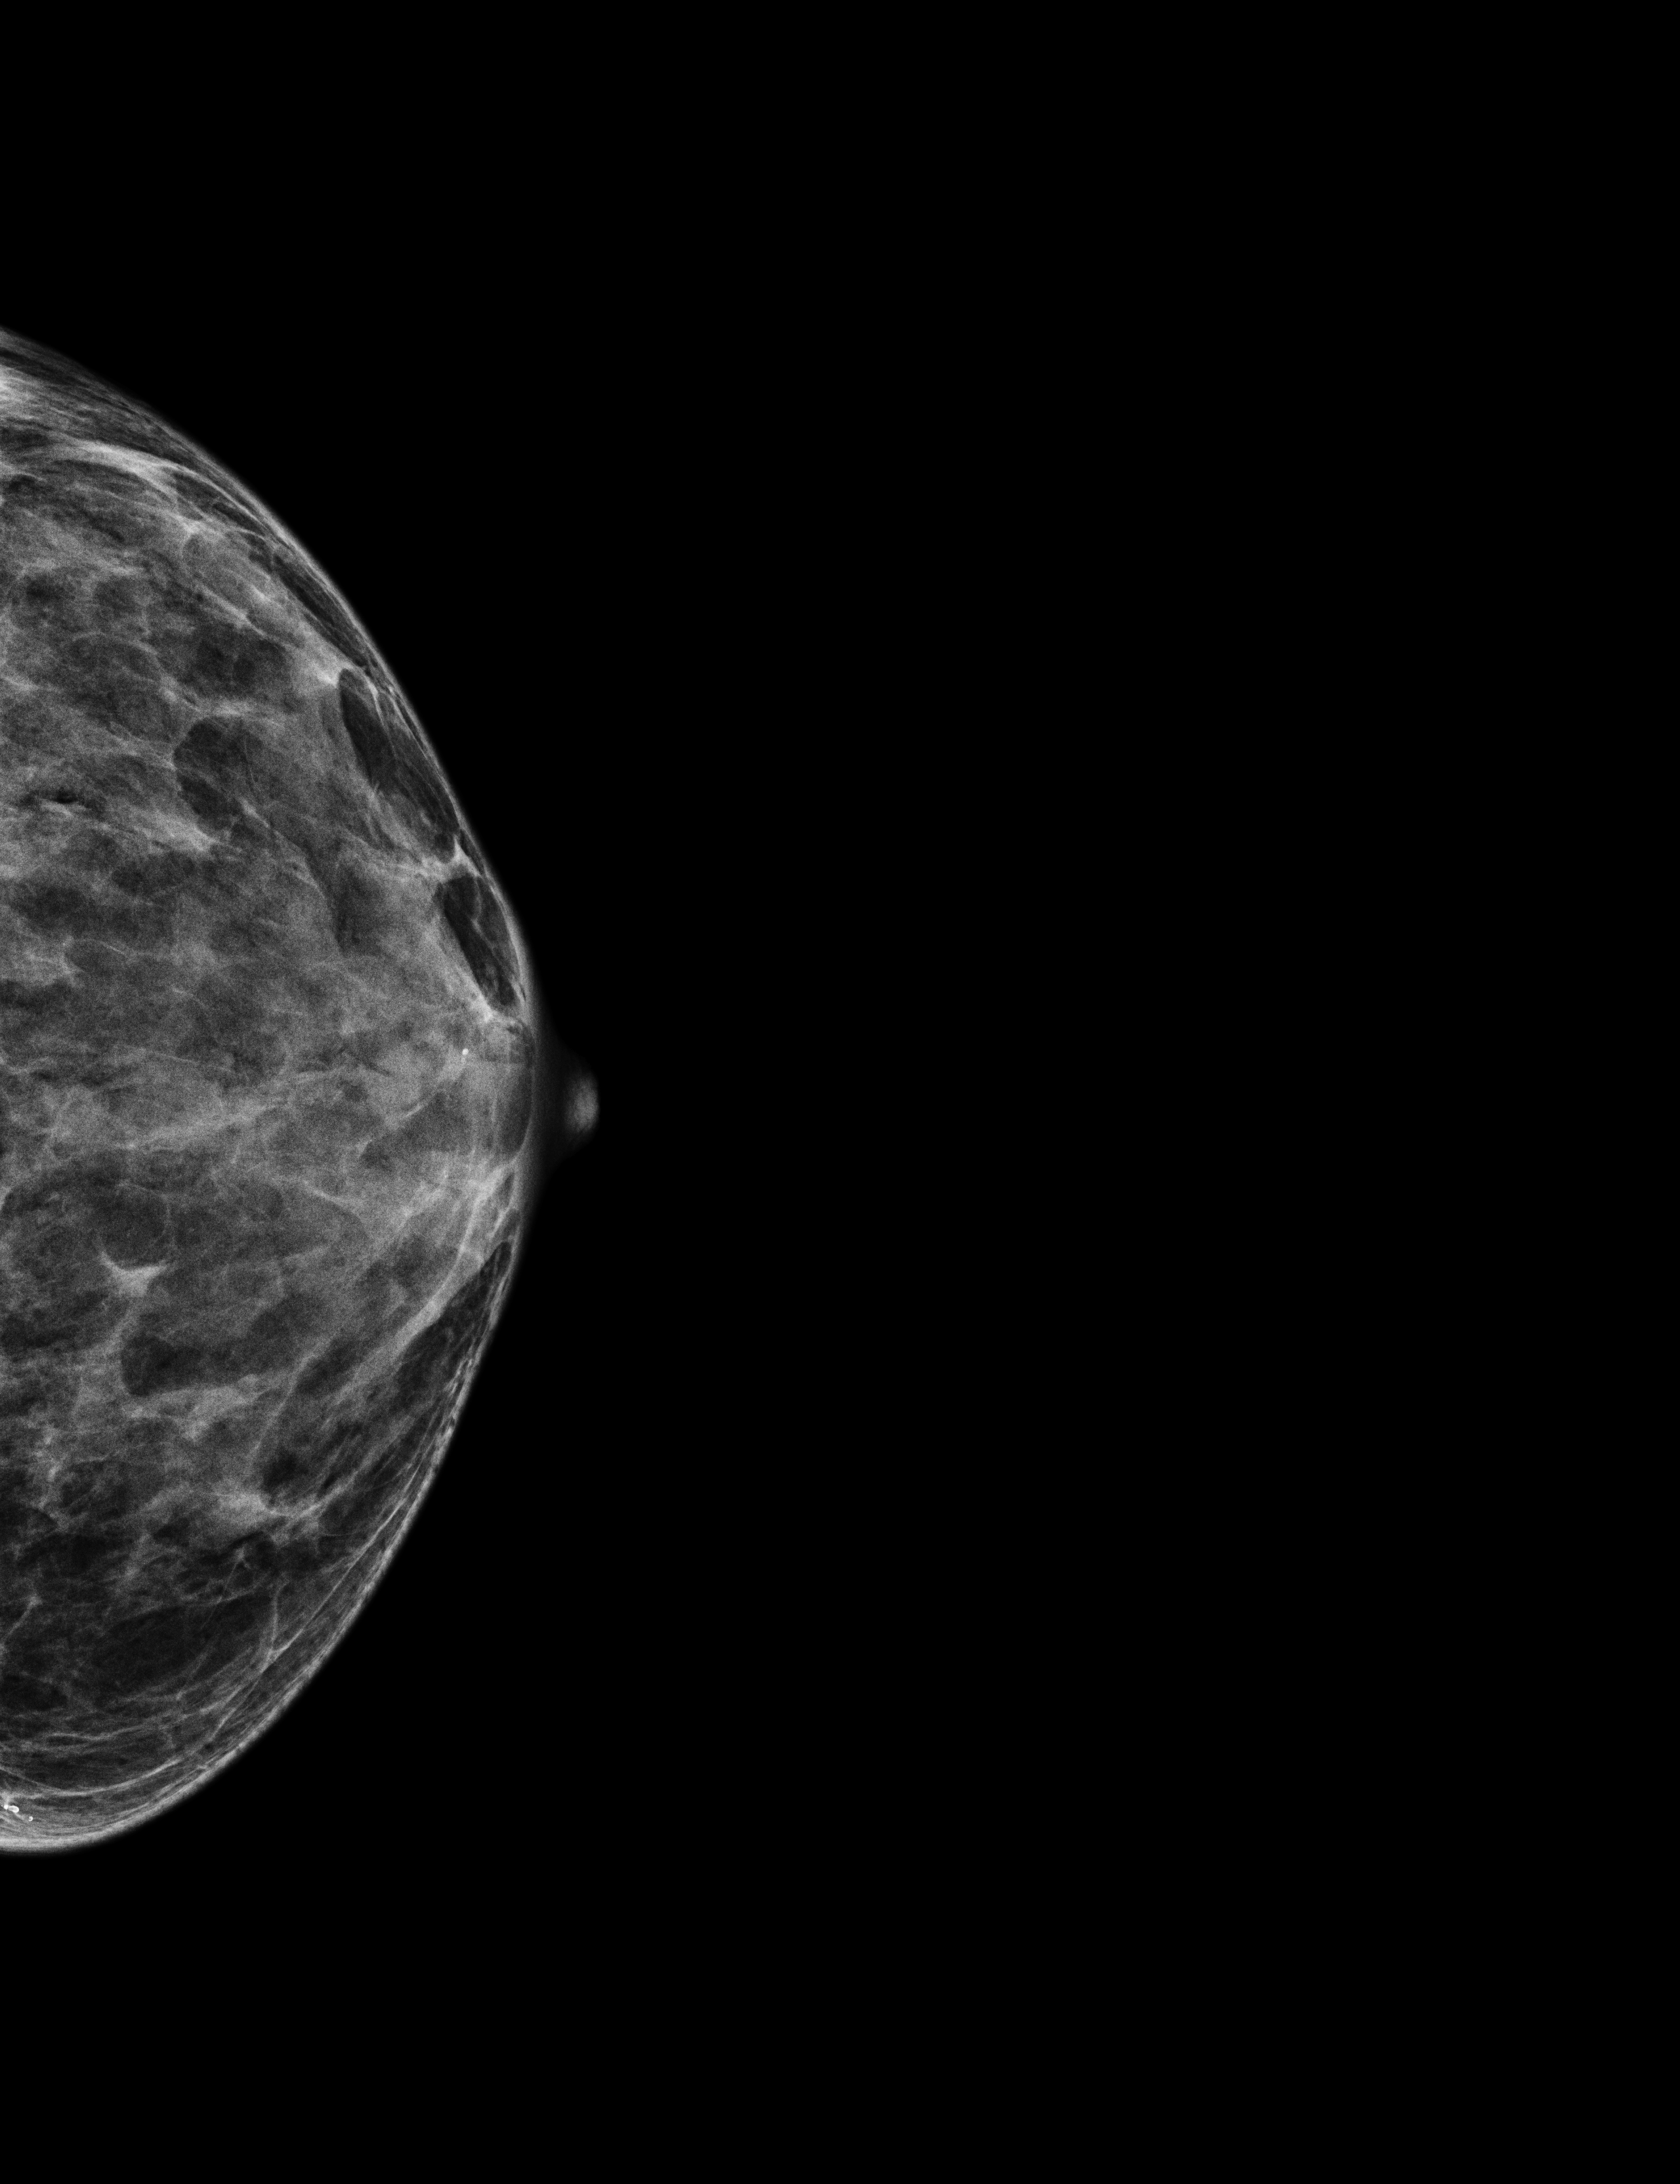
Full-field digital mammogram (FFDM); left breast; cranio-caudal projection; screening examination. Patient aged 68 years (female).
BI-RADS breast density category at the screening exam (both breasts, scale 1–4): 4. Final BI-RADS assessment for this screening round (tomosynthesis exam, both breasts): category 1. Recall: no recall after this screen.